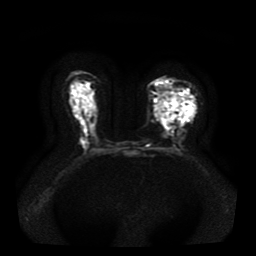
Breast MRI, one axial slice. Slice 23 of 41 in the series (ordered by position). Diffusion-weighted series; image 2 of 4 stored at this slice position (different b-values; order by instance number). 1.5 T. 5 mm slice thickness. 256 × 256 image matrix, field of view 330 × 330 mm. Female patient.
Annotated regions visible in this slice (manually delineated by an expert):
- tumour on diffusion-weighted imaging: bounding box (x1, y1, x2, y2) in pixels: (154, 92, 189, 123)